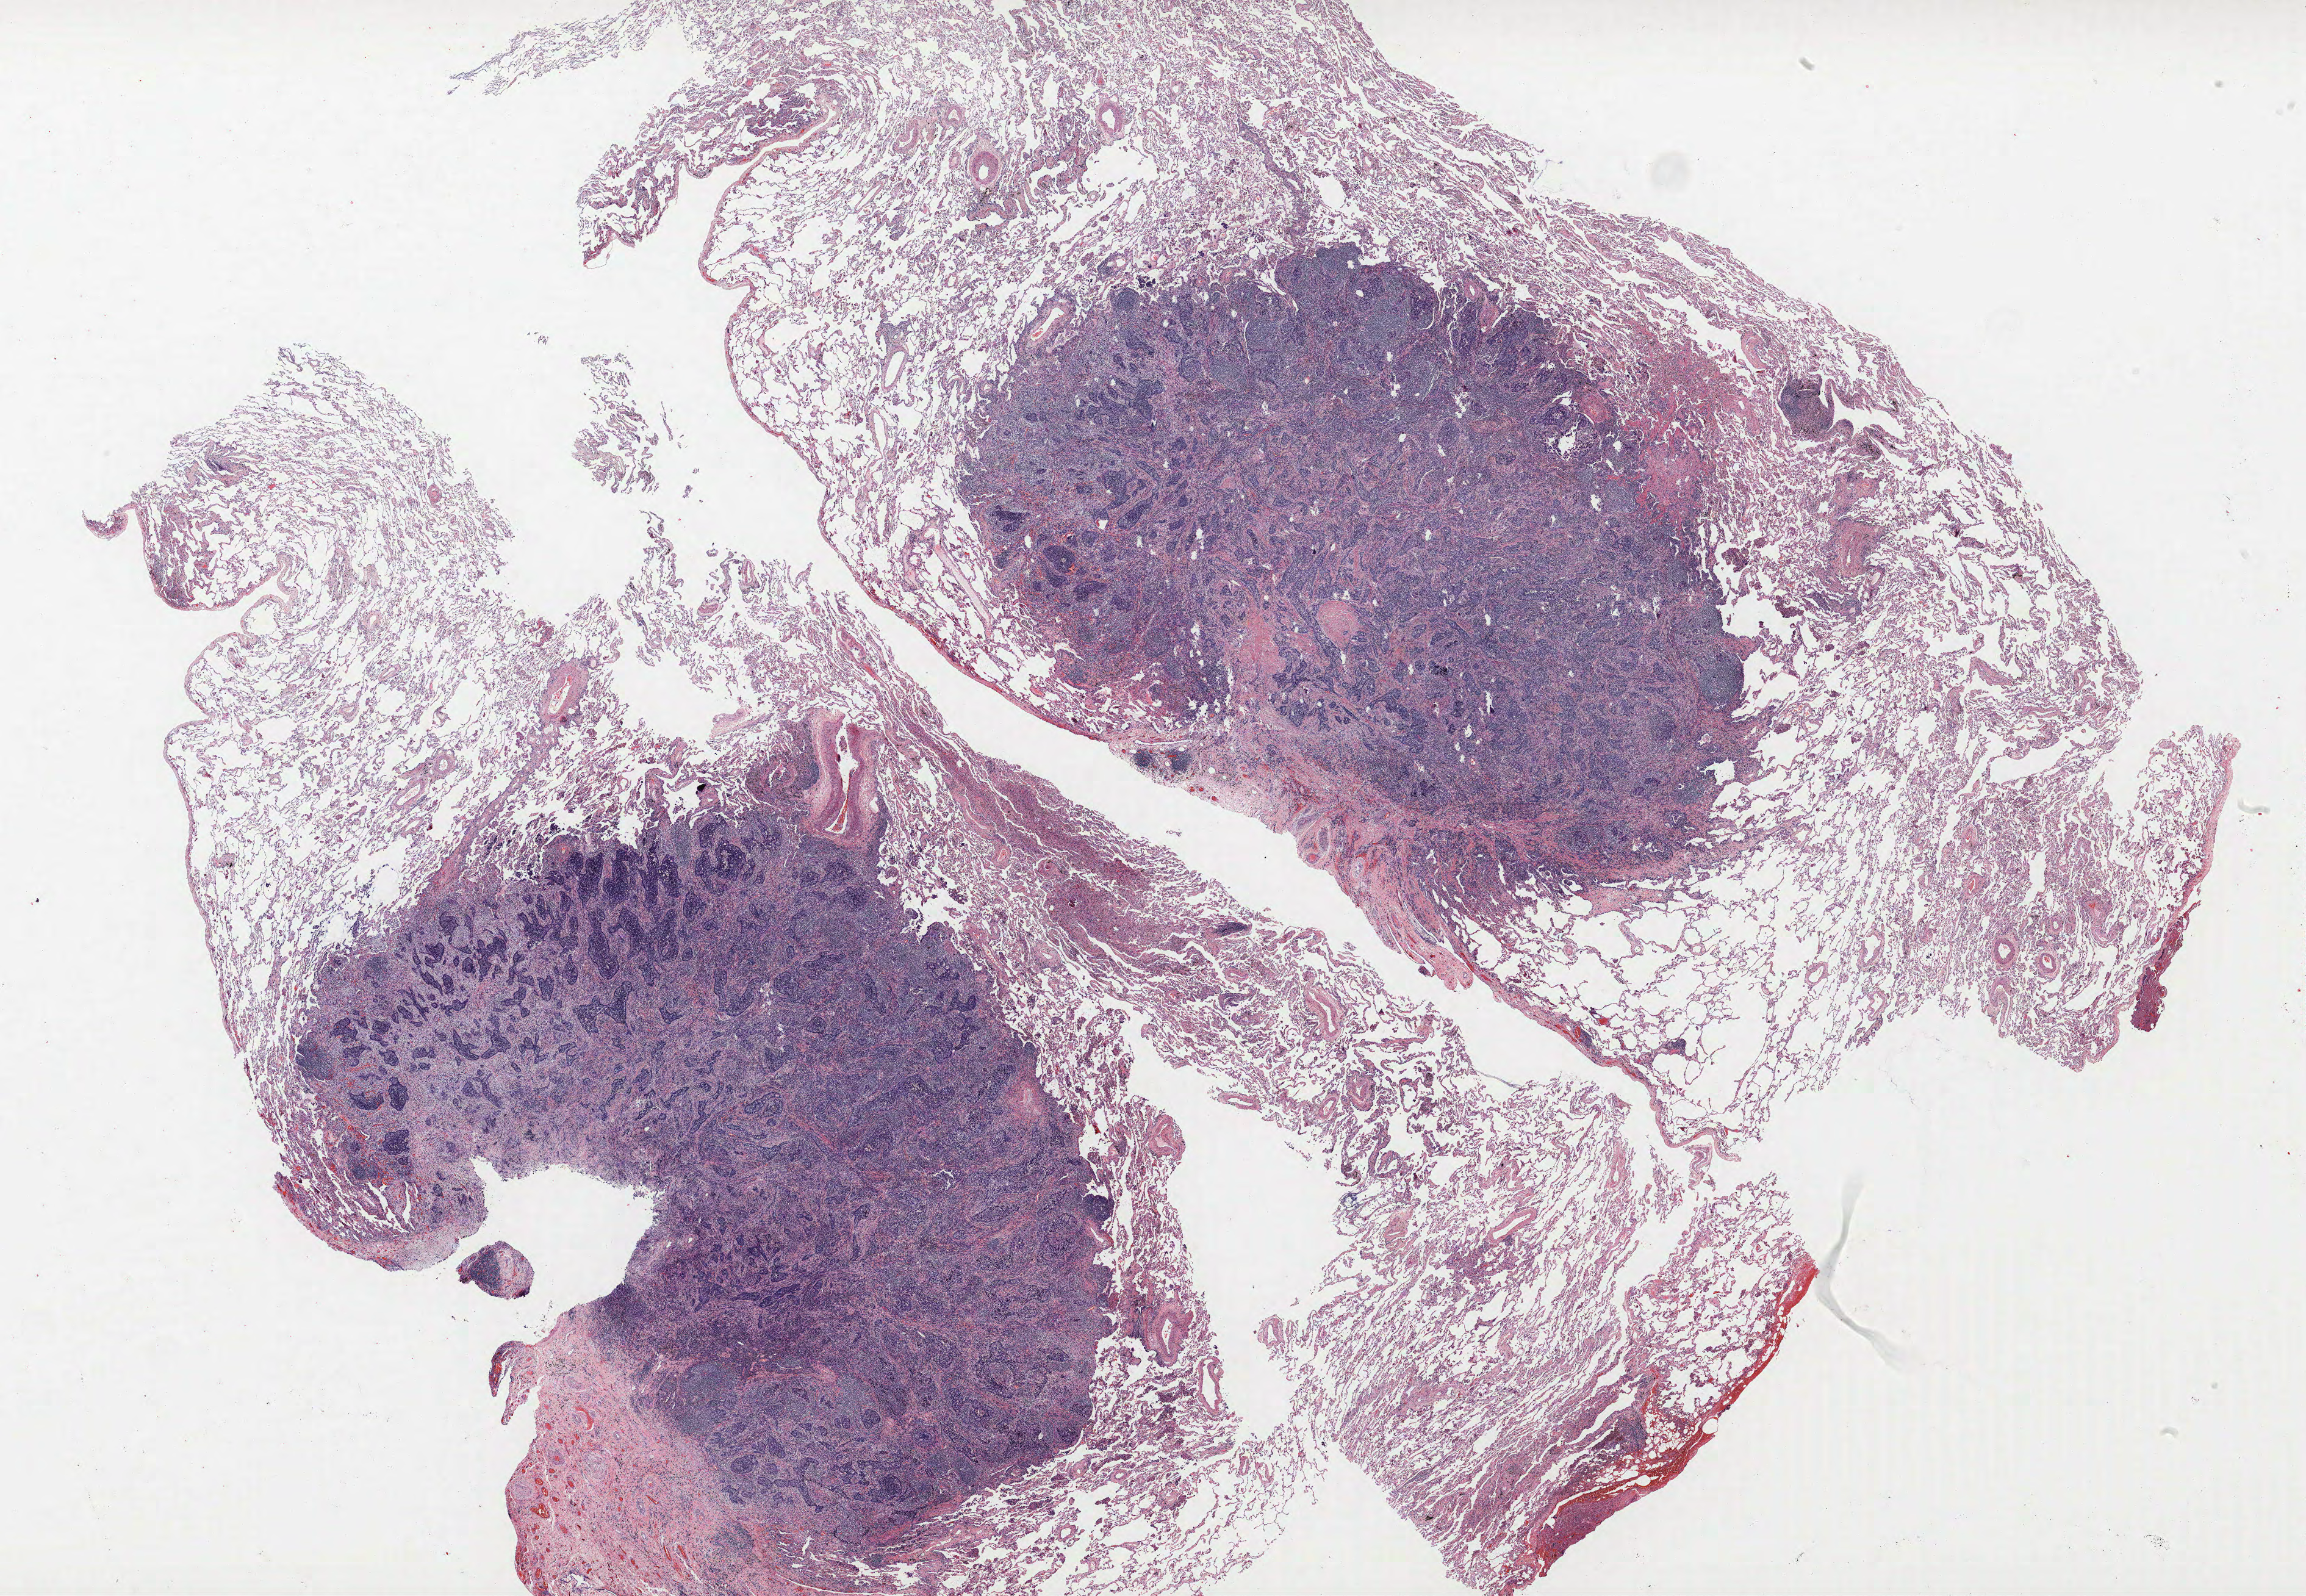
H&E-stained whole-slide image, a low-resolution overview of the entire scanned area, about 30.2 x 20.9 mm; FFPE section; lung. Female patient, aged 59 at enrolment. Current smoker at enrolment. Grade: poorly differentiated (G3).
Participant's lung-cancer diagnosis: Large cell neuroendocrine carcinoma (ICD-O-3 8013/3). Tumour size (pathology): 12 mm. Primary tumour location (clinical record): left upper lobe. Stage (AJCC 6th edition): IA.